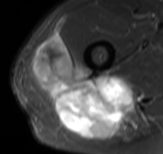
MRI of an extremity soft-tissue mass, one axial slice; position 60 of 61 along the scan axis; STIR; MR volume resampled by the dataset authors to the PET/CT grid (not the native acquisition matrix); 3.27 mm slice thickness; 163 × 154 image matrix, field of view 159 × 150 mm. Male patient. From the clinical record (not read from this slice): histological type: poorly differentiated synovial sarcoma; grade: high; site of the primary tumour: right buttock.
Structures marked on this image (expert contour drawn on MRI and transferred to this co-registered scan by the dataset authors):
- gross tumour volume including surrounding oedema: bounding box (x1, y1, x2, y2) in pixels: (30, 34, 147, 140)
- gross tumour volume (mass): (30, 34, 133, 140)